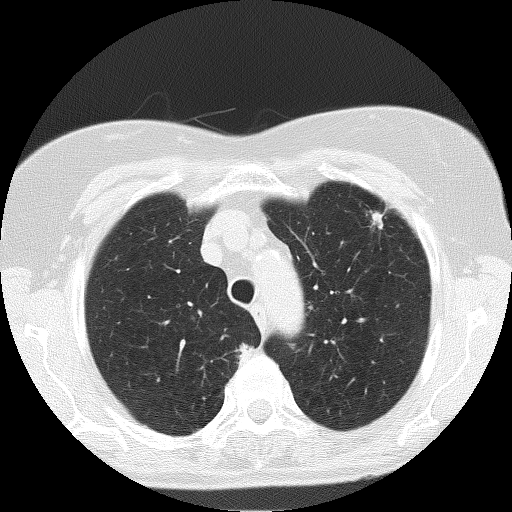
Low-dose screening chest CT, one axial slice. Position 135 of 166 along the scan axis. Lung window (W 1500 / L -600 HU). 512 × 512 image matrix.
Structures marked on this image (outlined manually by an expert reader):
- lesion 1 (tumor, upper lobe of left lung): bounding box [x1, y1, x2, y2] px = [372, 212, 383, 227]